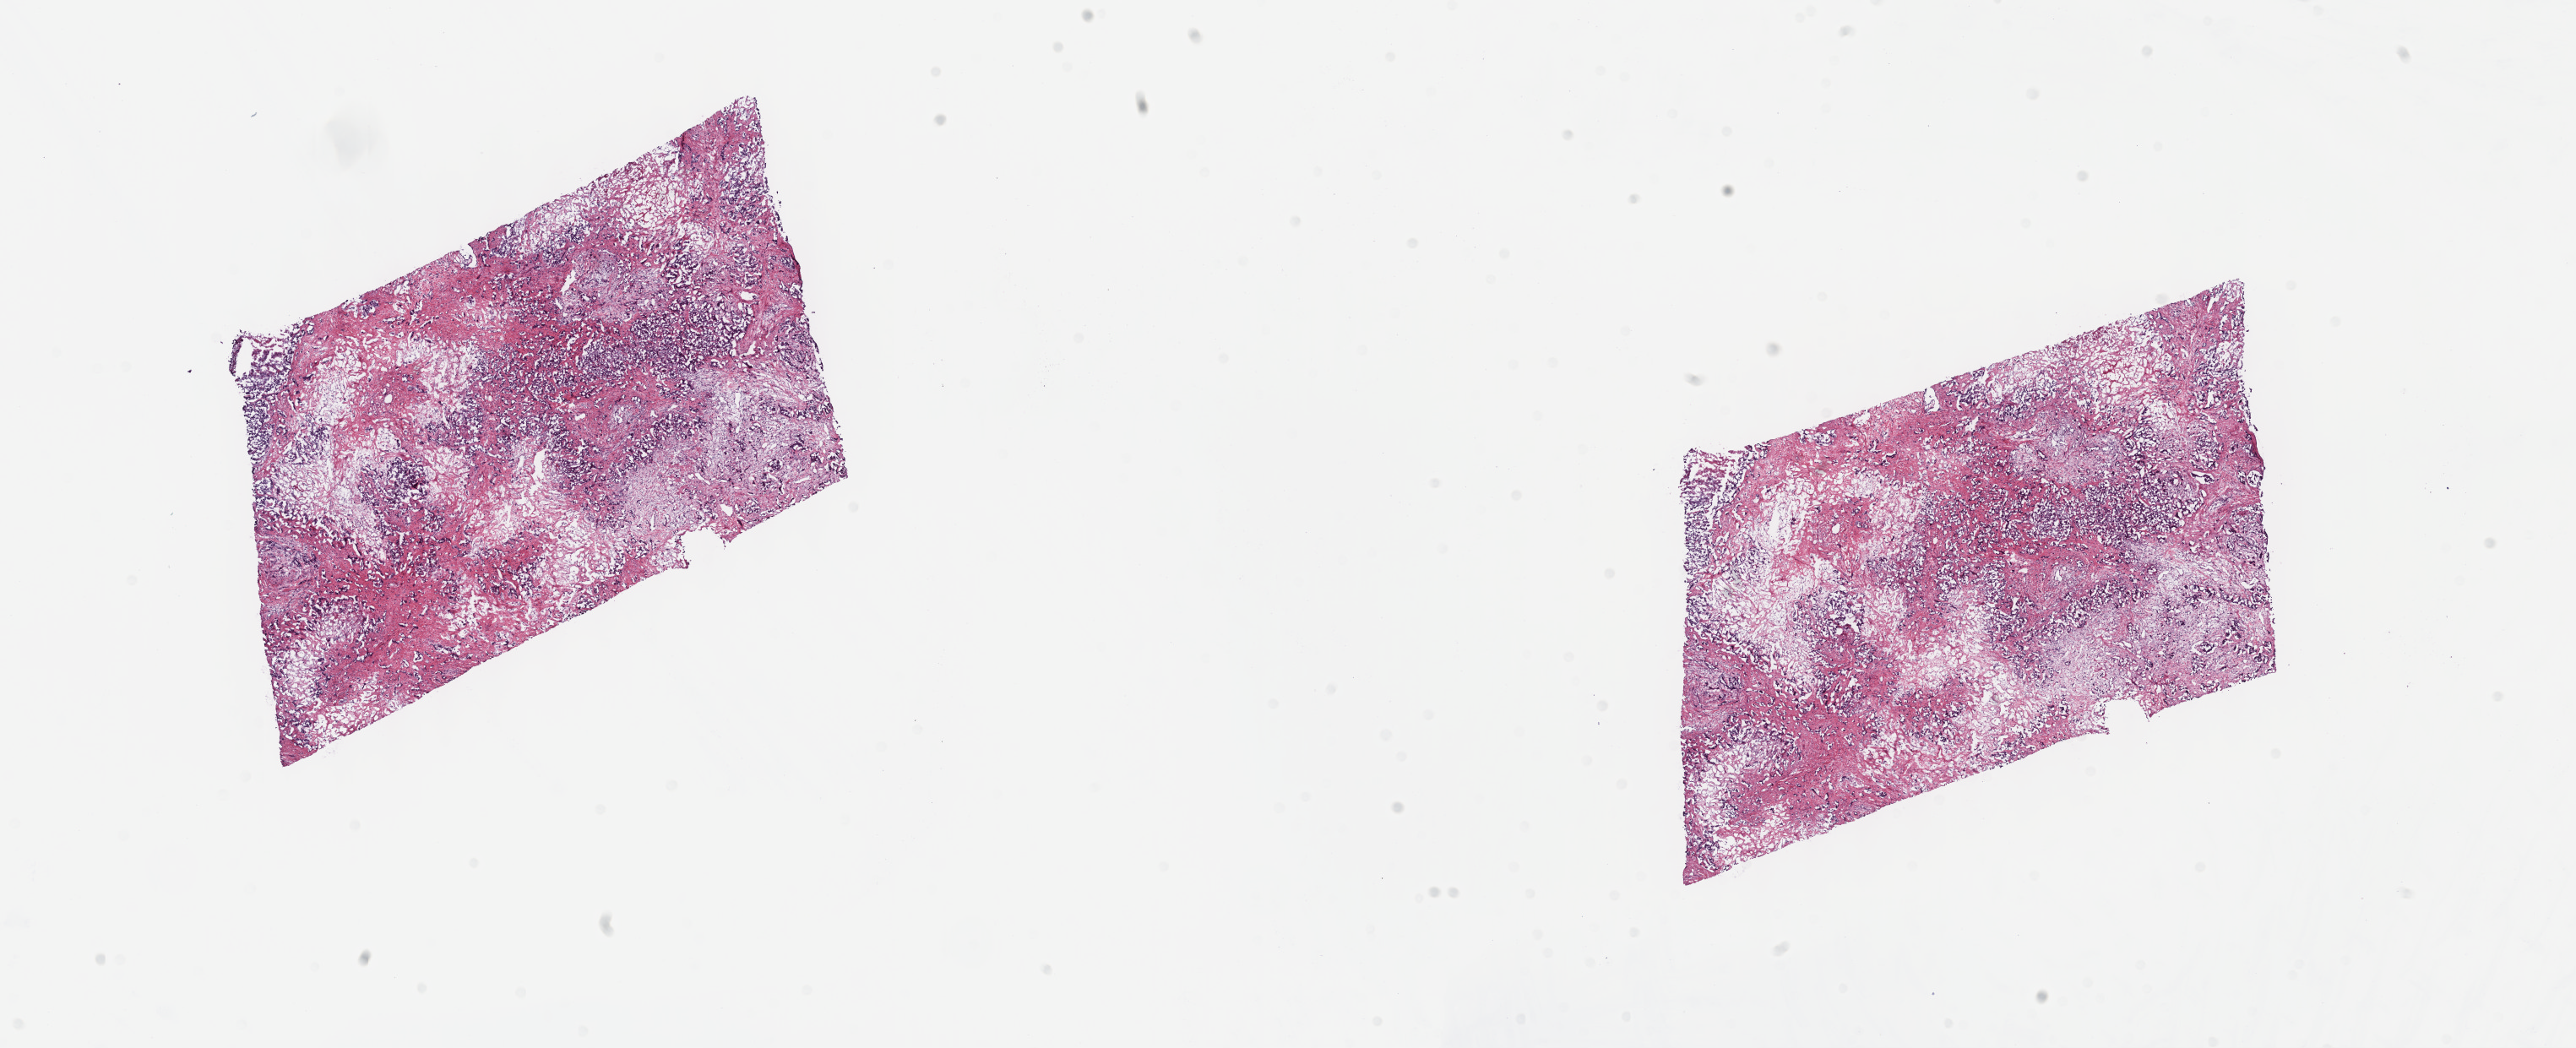
Hematoxylin and eosin (H&E) stained whole-slide image — whole scanned area (about 24.7 x 10.0 mm) shown as a low-resolution overview. Frozen section from the top of the tissue portion. Primary tumour sample from the bile duct. Patient: female, age at initial diagnosis 73 years. Histologic grade: G3 (poorly differentiated). Composition of this section per pathologist review: tumour cells 23%, tumour nuclei 75%, normal cells 0%, stromal cells 72%, necrosis 5%. Inflammatory infiltration, as recorded: lymphocyte infiltration 15%, monocyte infiltration 2%, neutrophil infiltration 2%.
* histologic diagnosis: Cholangiocarcinoma (intrahepatic bile duct)
* AJCC pathologic stage: II (7th edition)